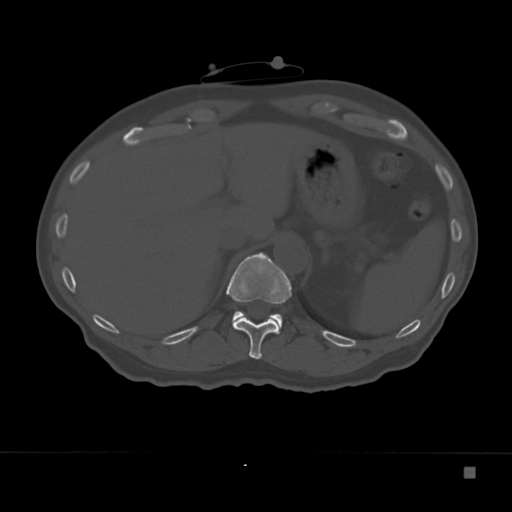
CT including the spine, one axial slice. Reconstruction kernel Br40s. 120 kVp. Bone window (W 1800 / L 400 HU). 512 × 512 image matrix, field of view 389 × 389 mm. Patient: male, 72 years. Case-level facts recorded for this patient, not image findings: primary cancer: skeletal.
Structures marked on this image (semi-automatically segmented with operator editing):
- T11 vertebra: bounding box (x1, y1, x2, y2) in pixels: (226, 252, 292, 359)
- T12 vertebra: (232, 311, 283, 332)